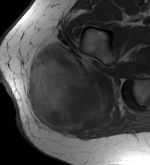
MRI of an extremity soft-tissue mass, one axial slice; slice 23 of 56 in the series (ordered by position); MR volume resampled by the dataset authors to the PET/CT grid (not the native acquisition matrix); 3.27 mm slice thickness; 150 × 165 image matrix. Female patient. Case-level facts recorded for this patient, not image findings: histological type: epithelioid sarcoma with vascular differentiation; site of the primary tumour: right buttock.
Outlined on this slice (expert contour drawn on MRI and transferred to this co-registered scan by the dataset authors):
- gross tumour volume (mass): bounding box (x1, y1, x2, y2) in pixels: (25, 44, 113, 135)